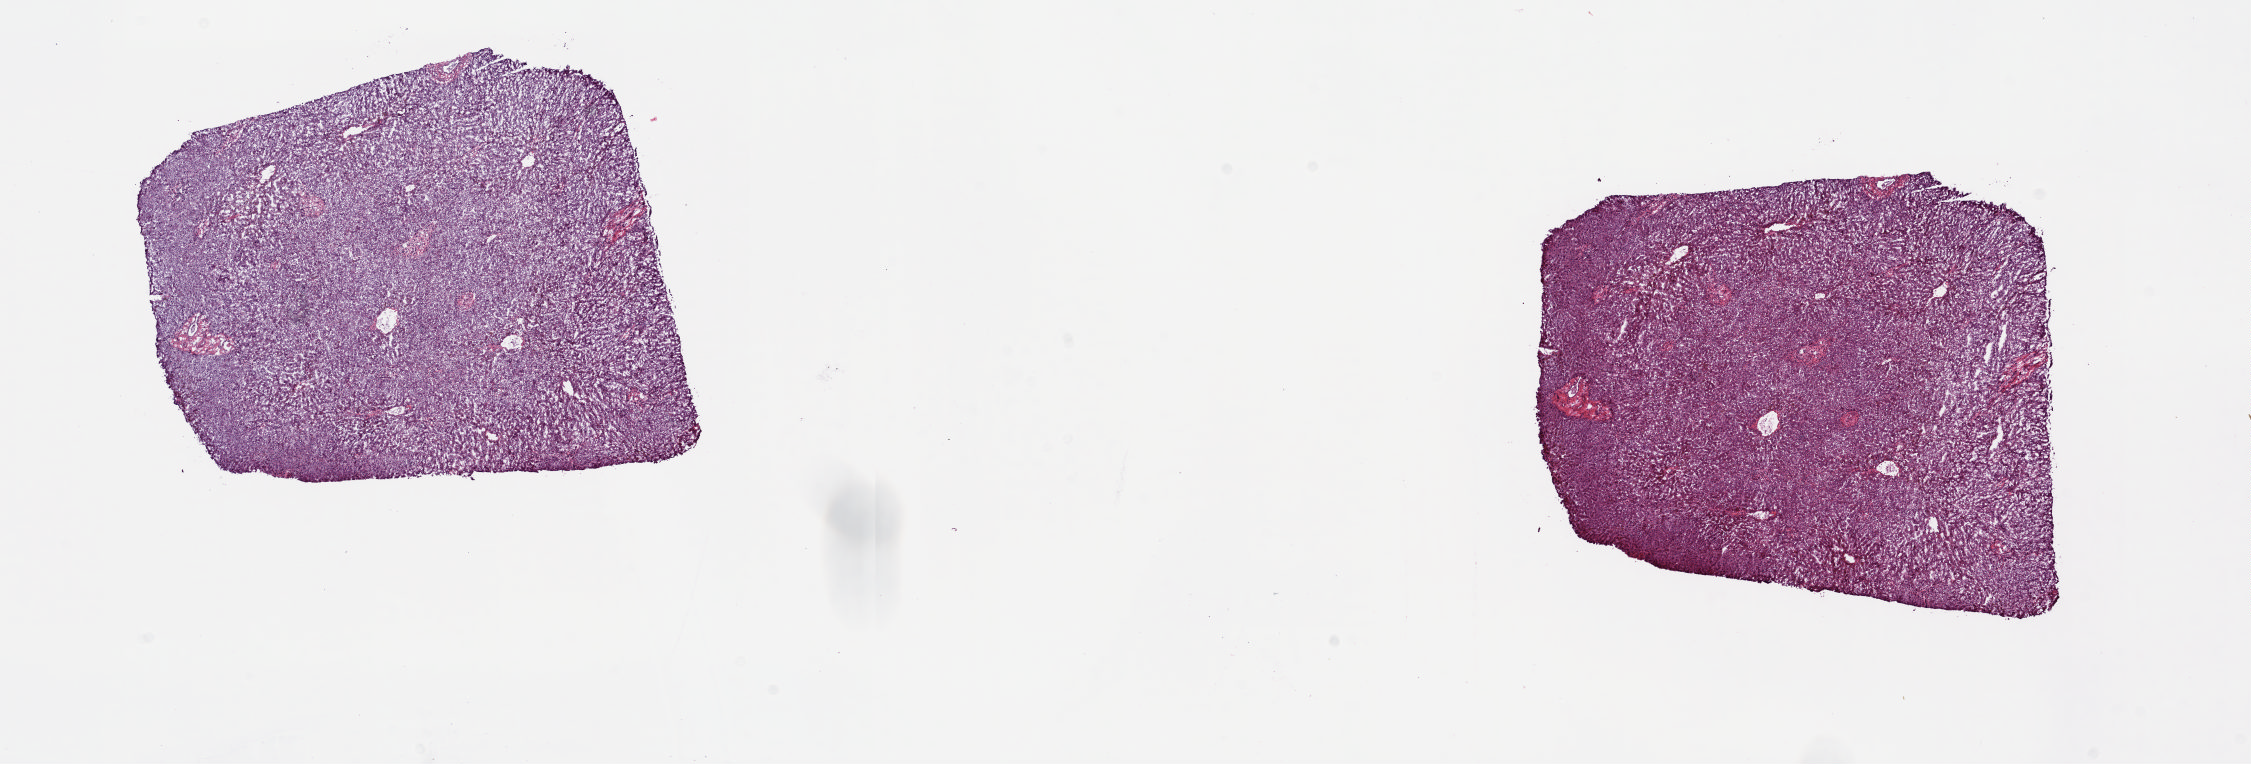
H&E-stained whole-slide image, low-resolution overview of the scanned area, about 17.9 x 6.1 mm (from a 20x scan); frozen section; bile duct, solid tissue normal (non-tumour tissue) sample. Male patient; age at initial diagnosis 82 years. Composition of this section per pathologist review: tumour cells 0%, tumour nuclei 0%, normal cells 100%, stromal cells 0%, necrosis 0%. Infiltration values recorded for this section: lymphocyte infiltration 2%, monocyte infiltration 0%, neutrophil infiltration 0%.
This section: solid tissue normal (non-tumour) sample from the same patient. Patient diagnosis: Cholangiocarcinoma (intrahepatic bile duct).